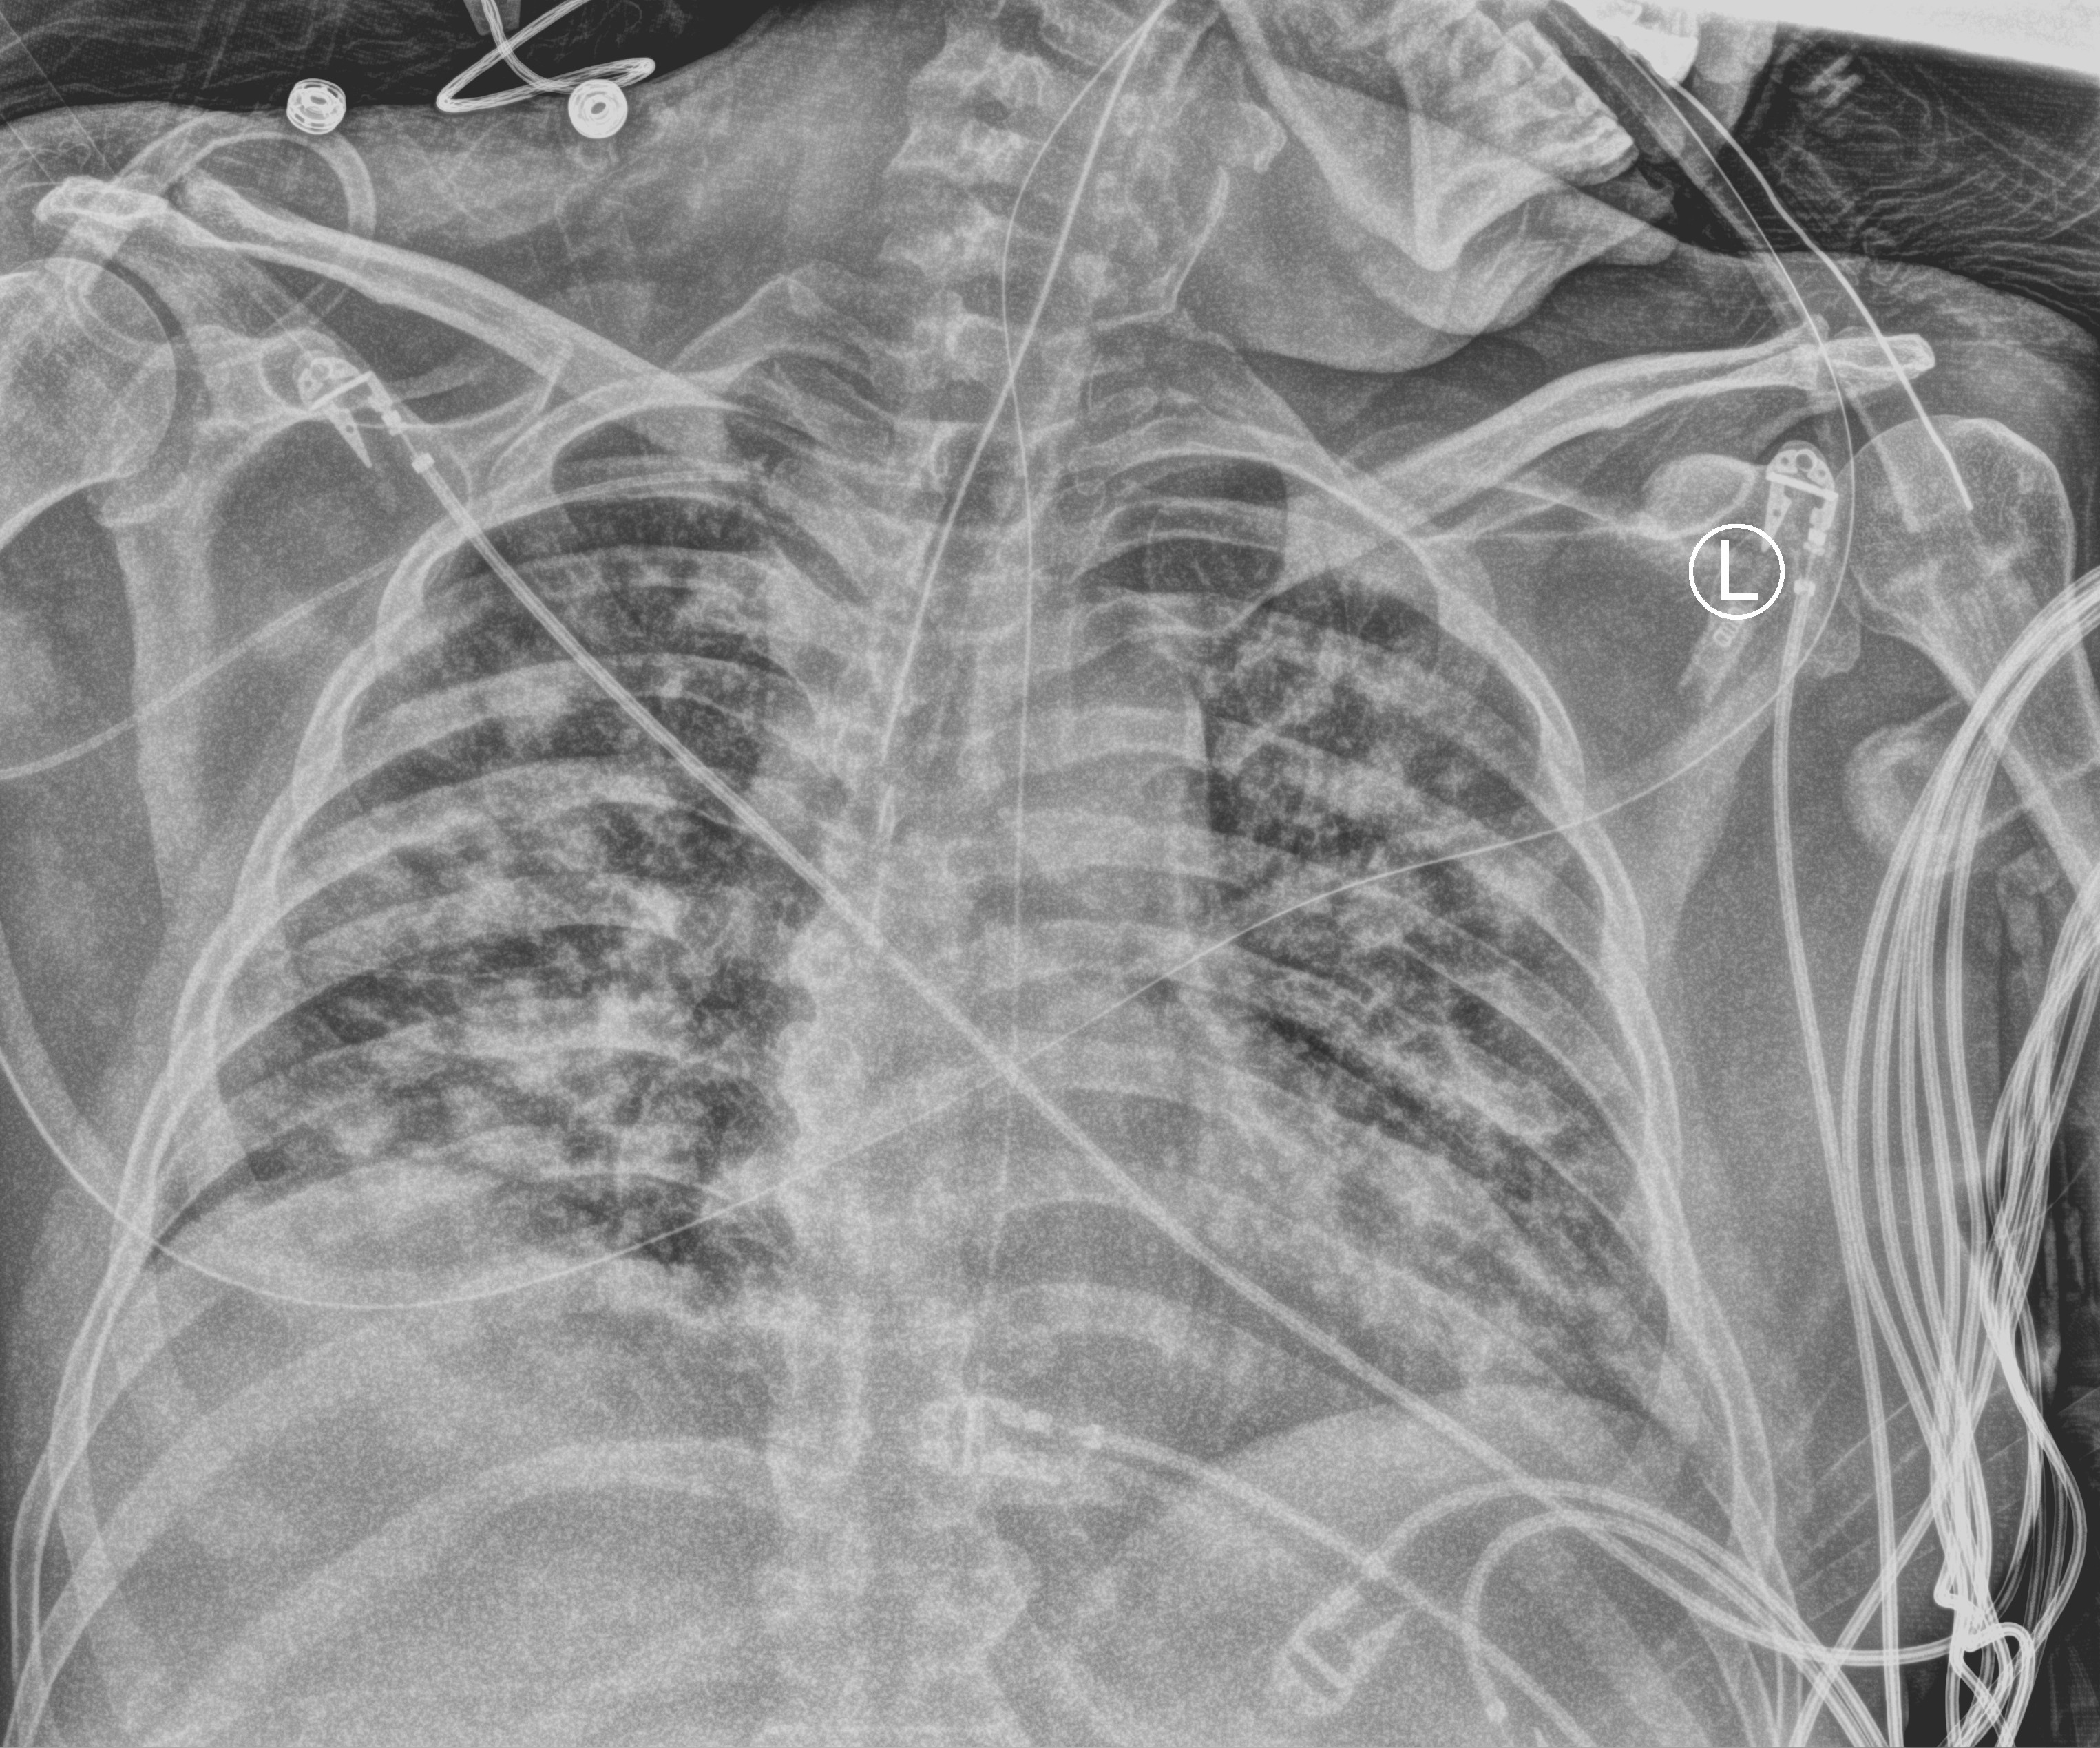
Portable chest radiograph; anteroposterior (AP) projection. Male patient hospitalised with COVID-19, age 18–59 years.
From the hospital-stay record, not from the radiograph (when in the stay this image was taken is not recorded): admitted to intensive care during this hospital stay: yes; mechanically ventilated during this hospital stay: yes.